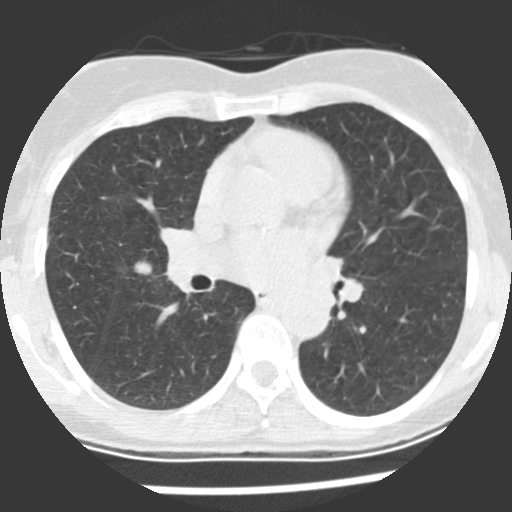
Low-dose screening chest CT, one axial slice; slice 117 of 225 in the series (ordered by position); reconstruction kernel STANDARD; 120 kVp; lung window (W 1500 / L -600 HU); 2.5 mm slice thickness; 512 × 512 image matrix.
Outlined on this slice (expert manual segmentation):
- lesion 1 (tumor, upper lobe of right lung): bounding box <135,261,152,274> (left, top, right, bottom; pixels)